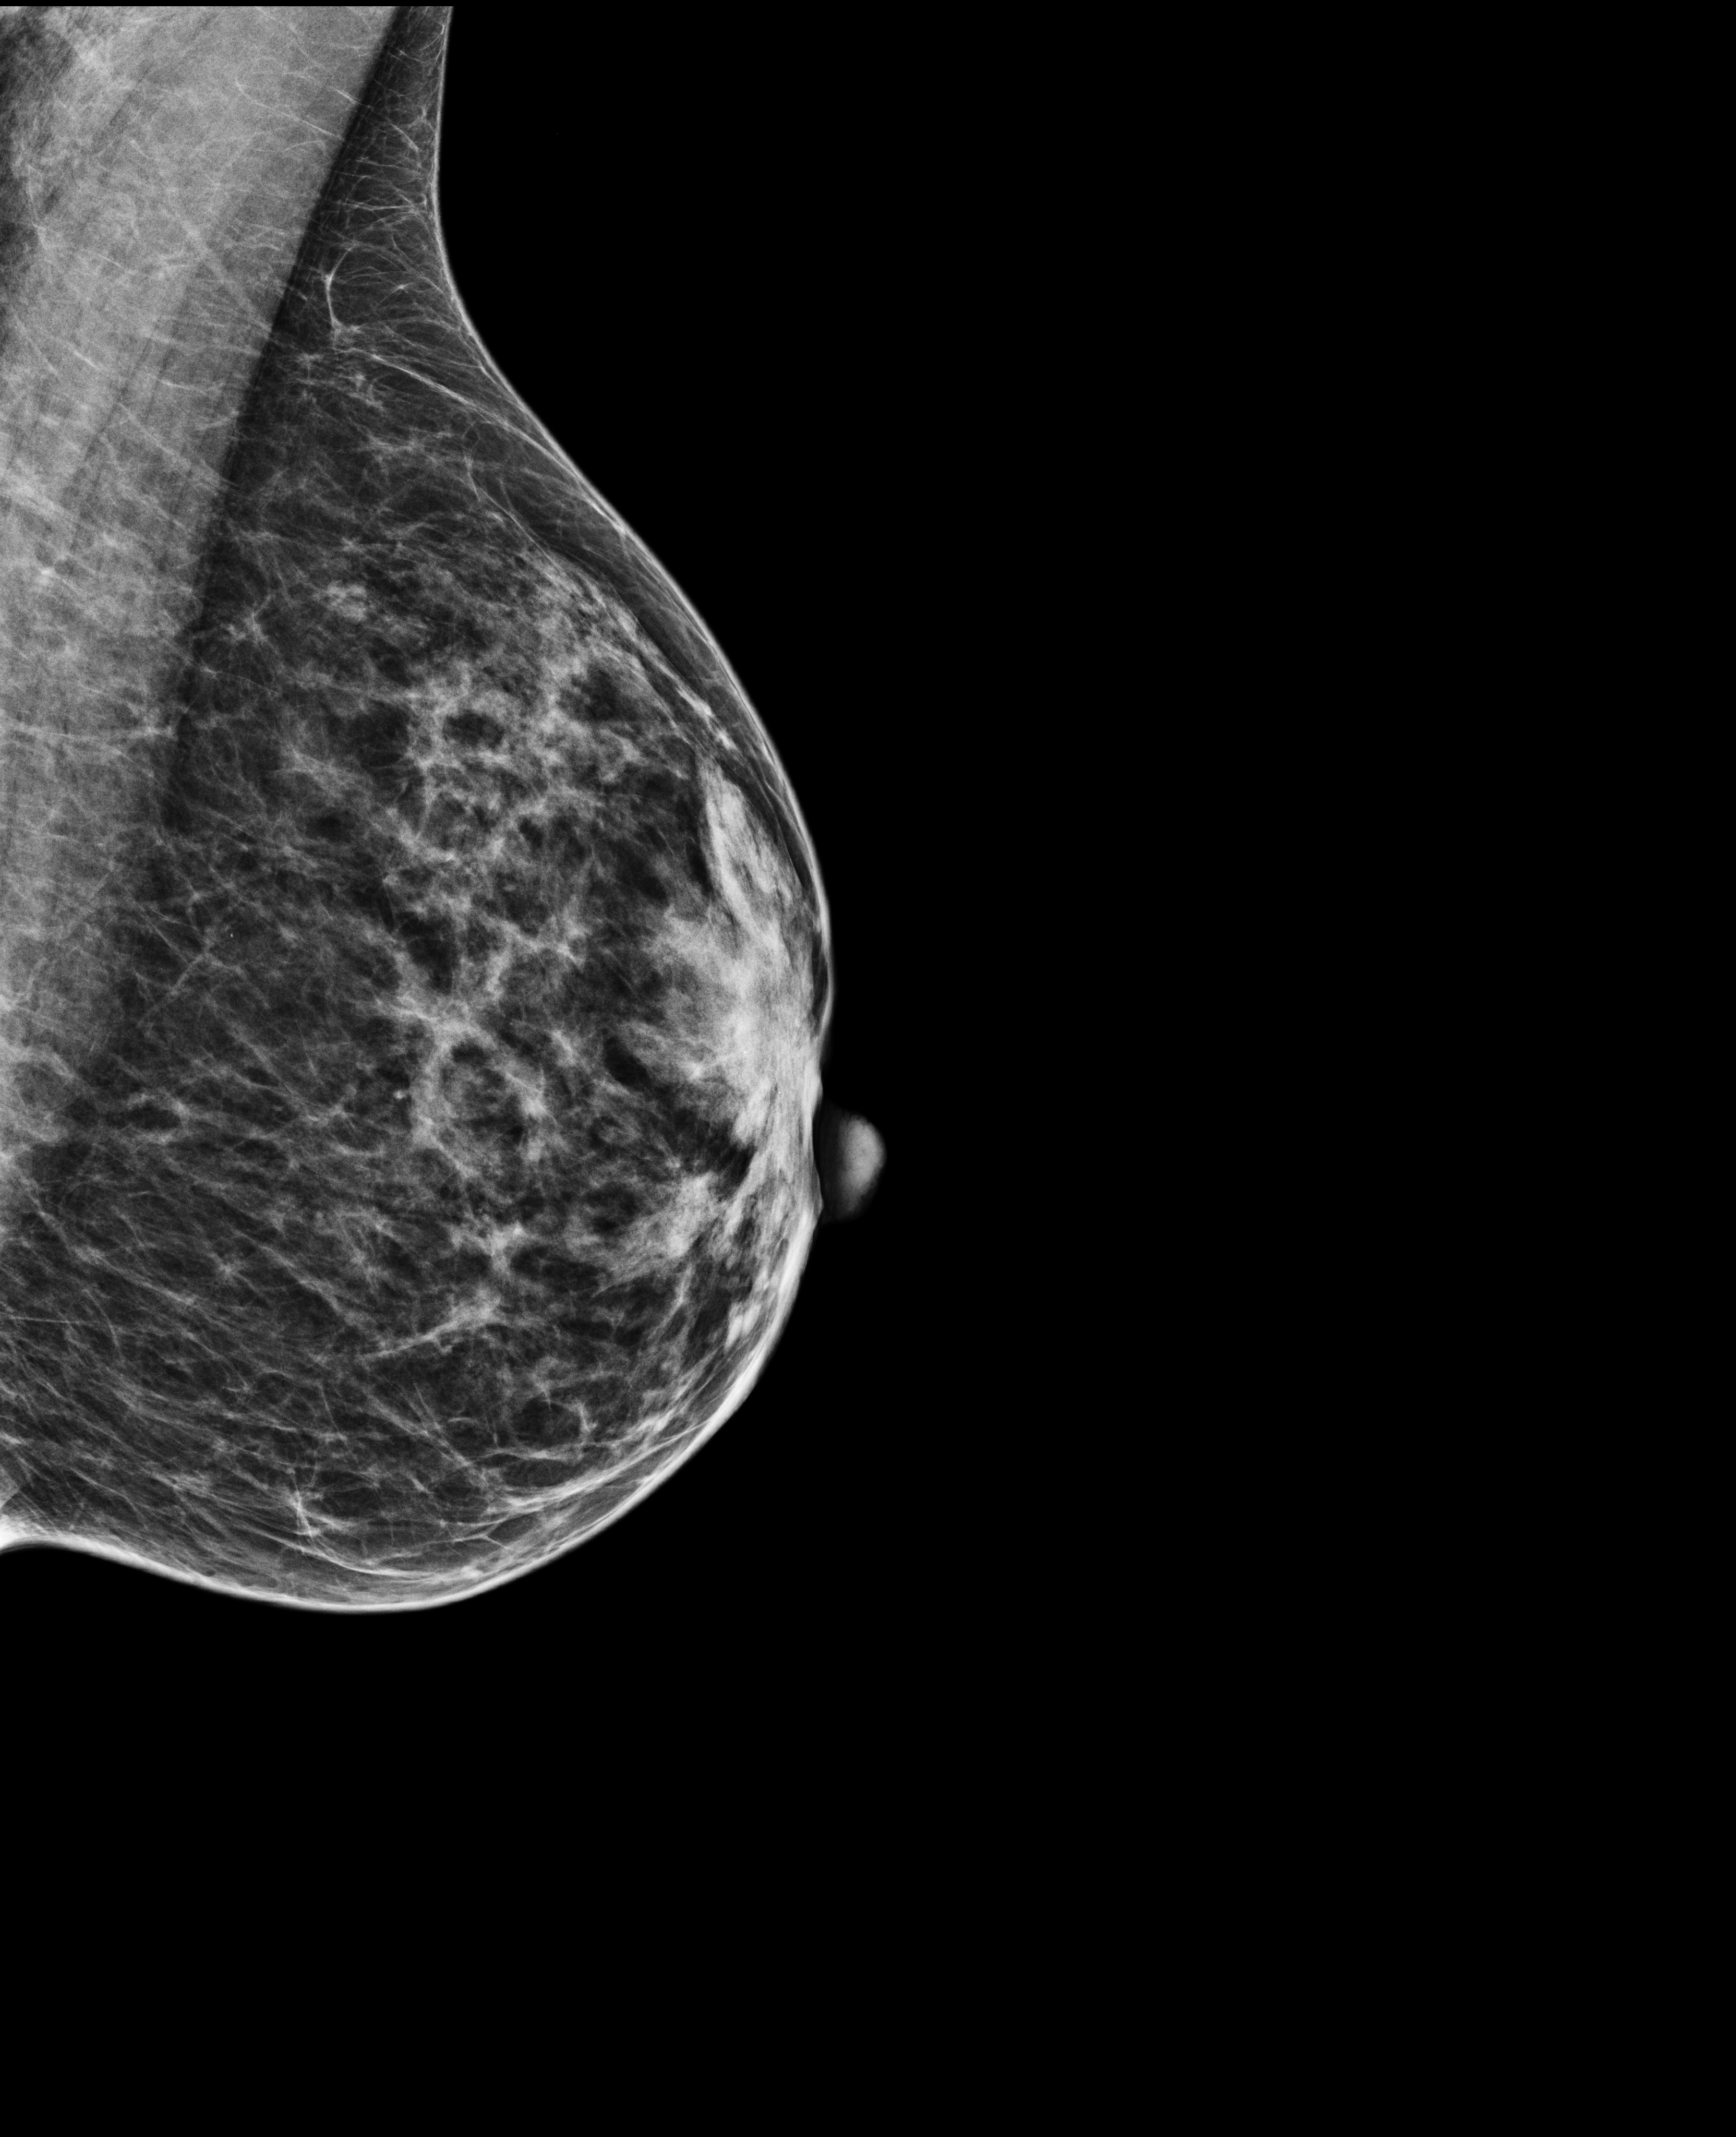
Screening examination; system: Selenia Dimensions. Patient aged 51 years (female).
Image type: full-field digital mammogram. Breast: left. Projection: mediolateral oblique (MLO) view.